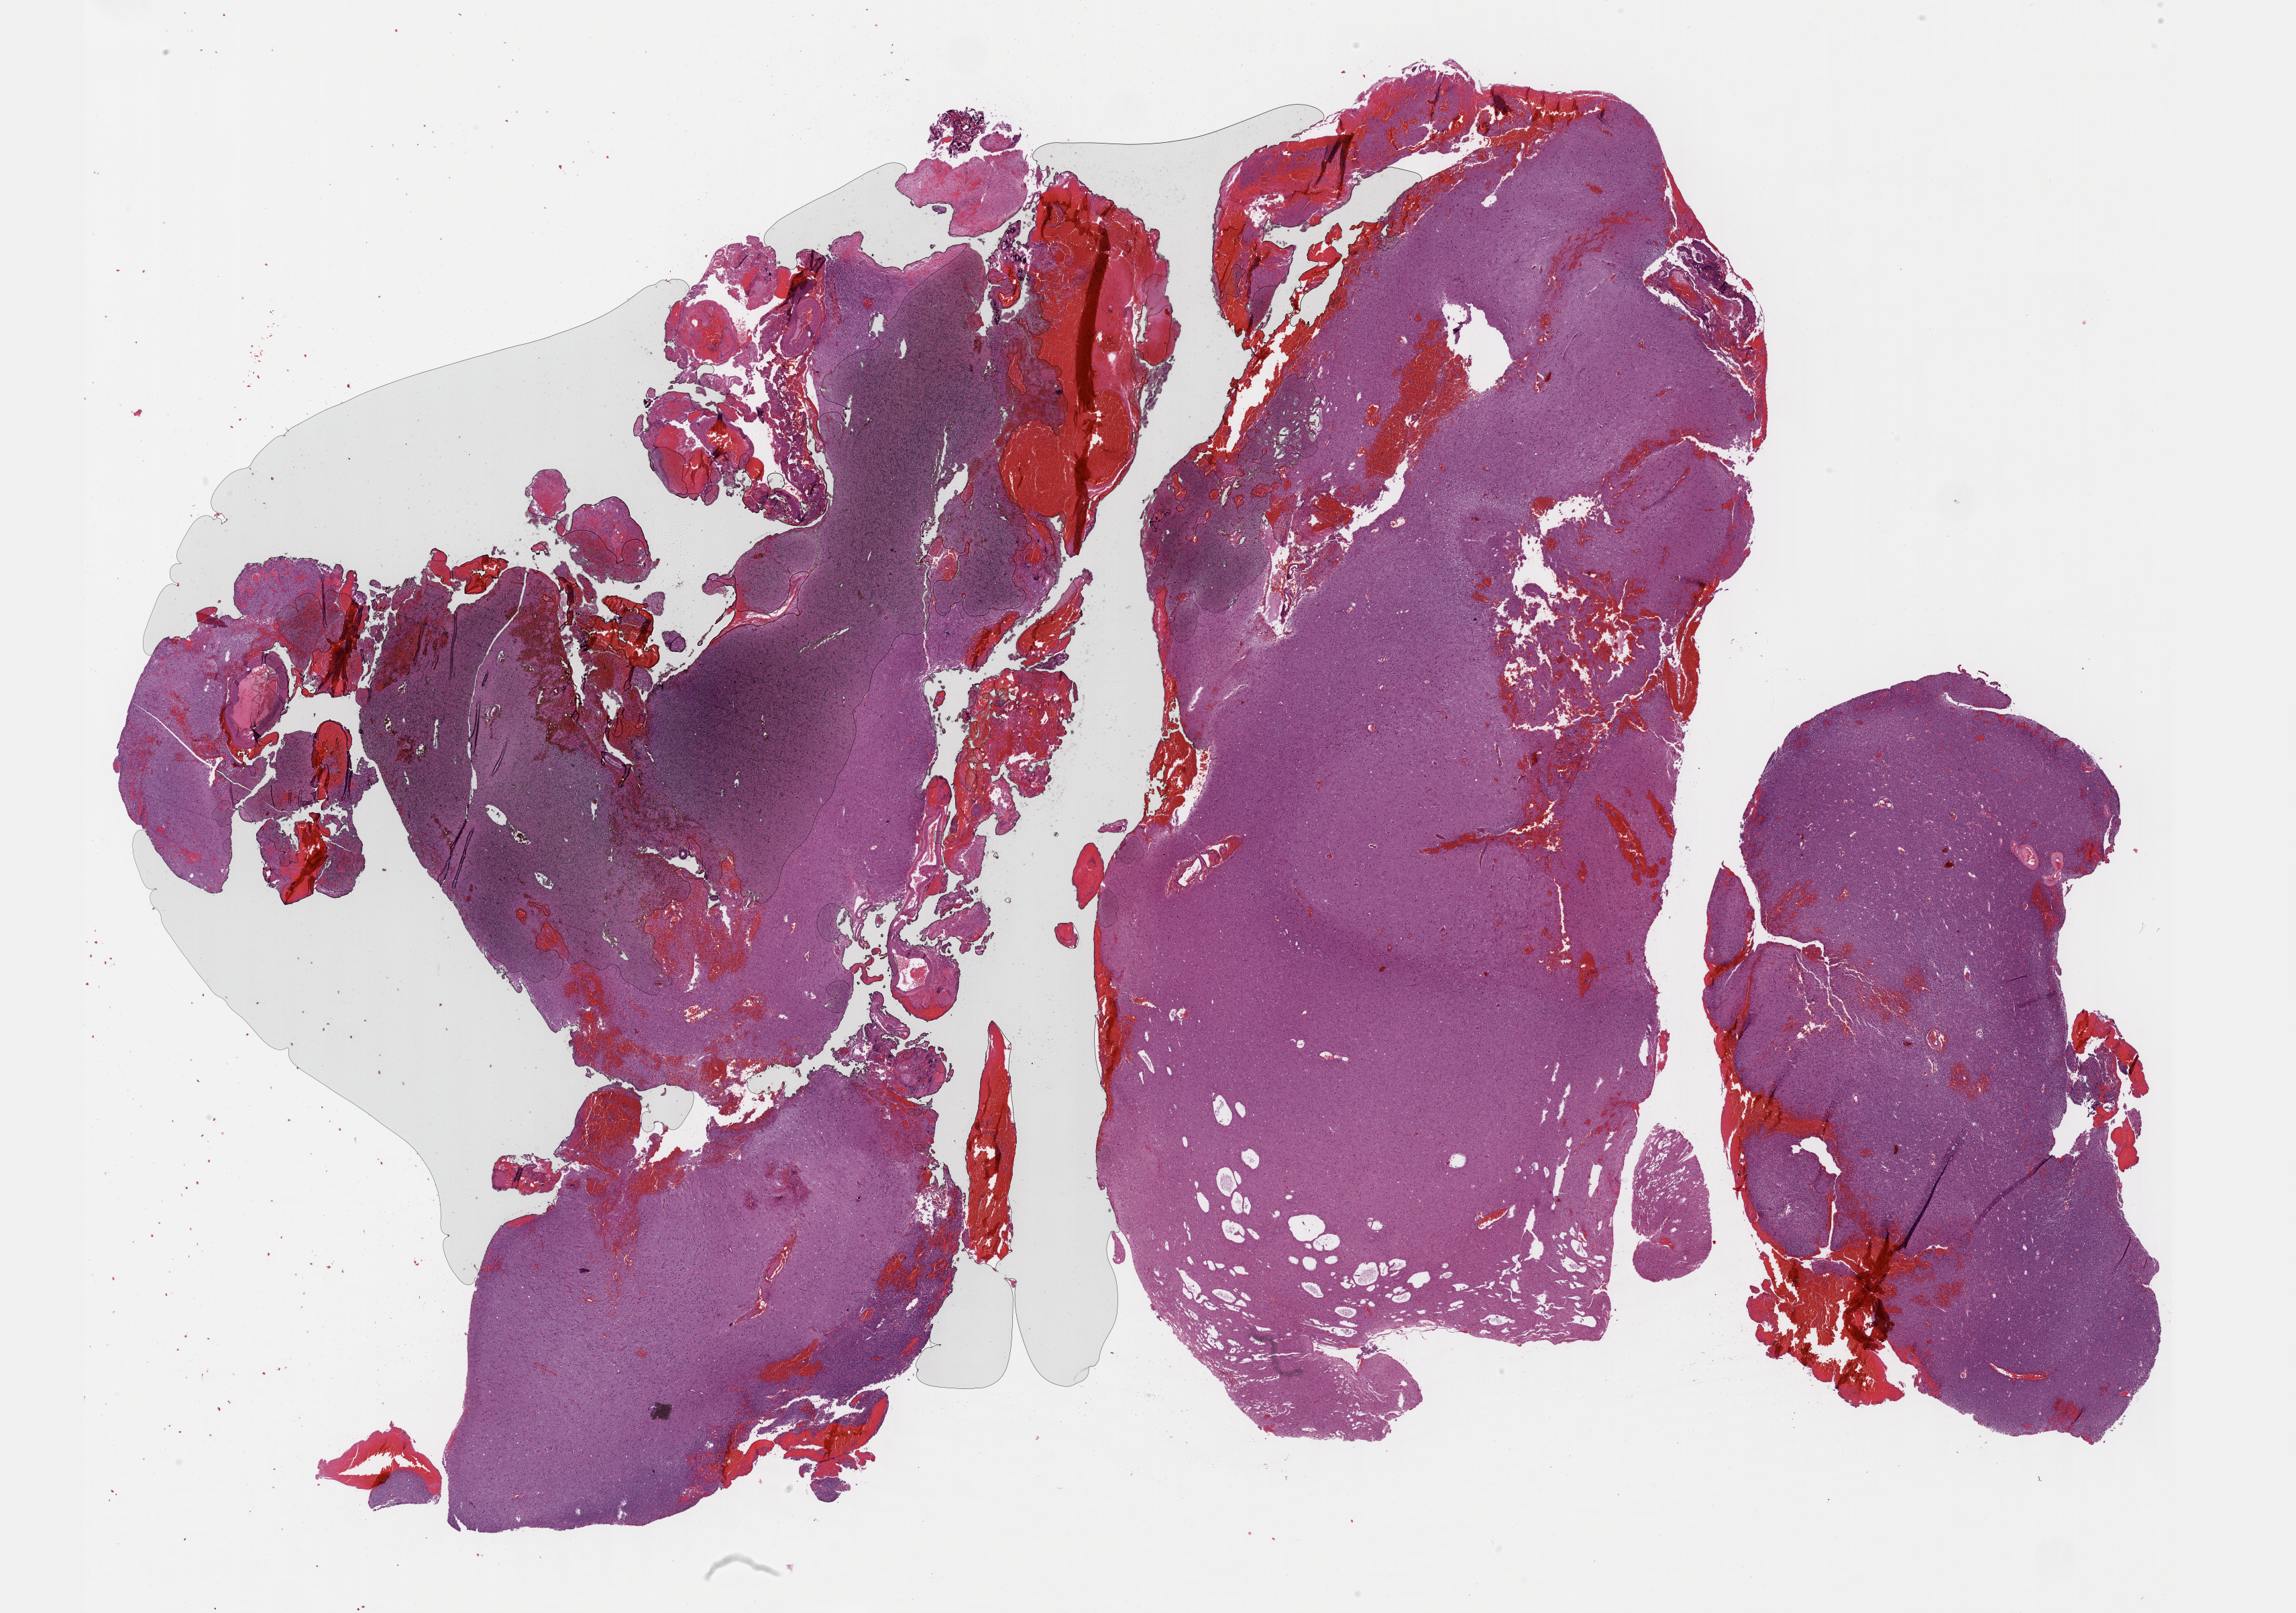
Whole-slide histology image, Hematoxylin and eosin (H&E) stained, whole scanned area (about 27.7 x 19.4 mm) shown as a low-resolution overview. Formalin-fixed paraffin-embedded (FFPE) diagnostic section. Sample: primary tumour, brain. Male patient; age at initial diagnosis 60 years. Histologic grade: G3 (poorly differentiated).
Histologic diagnosis: Oligodendroglioma, anaplastic (cerebrum). Laterality: right.